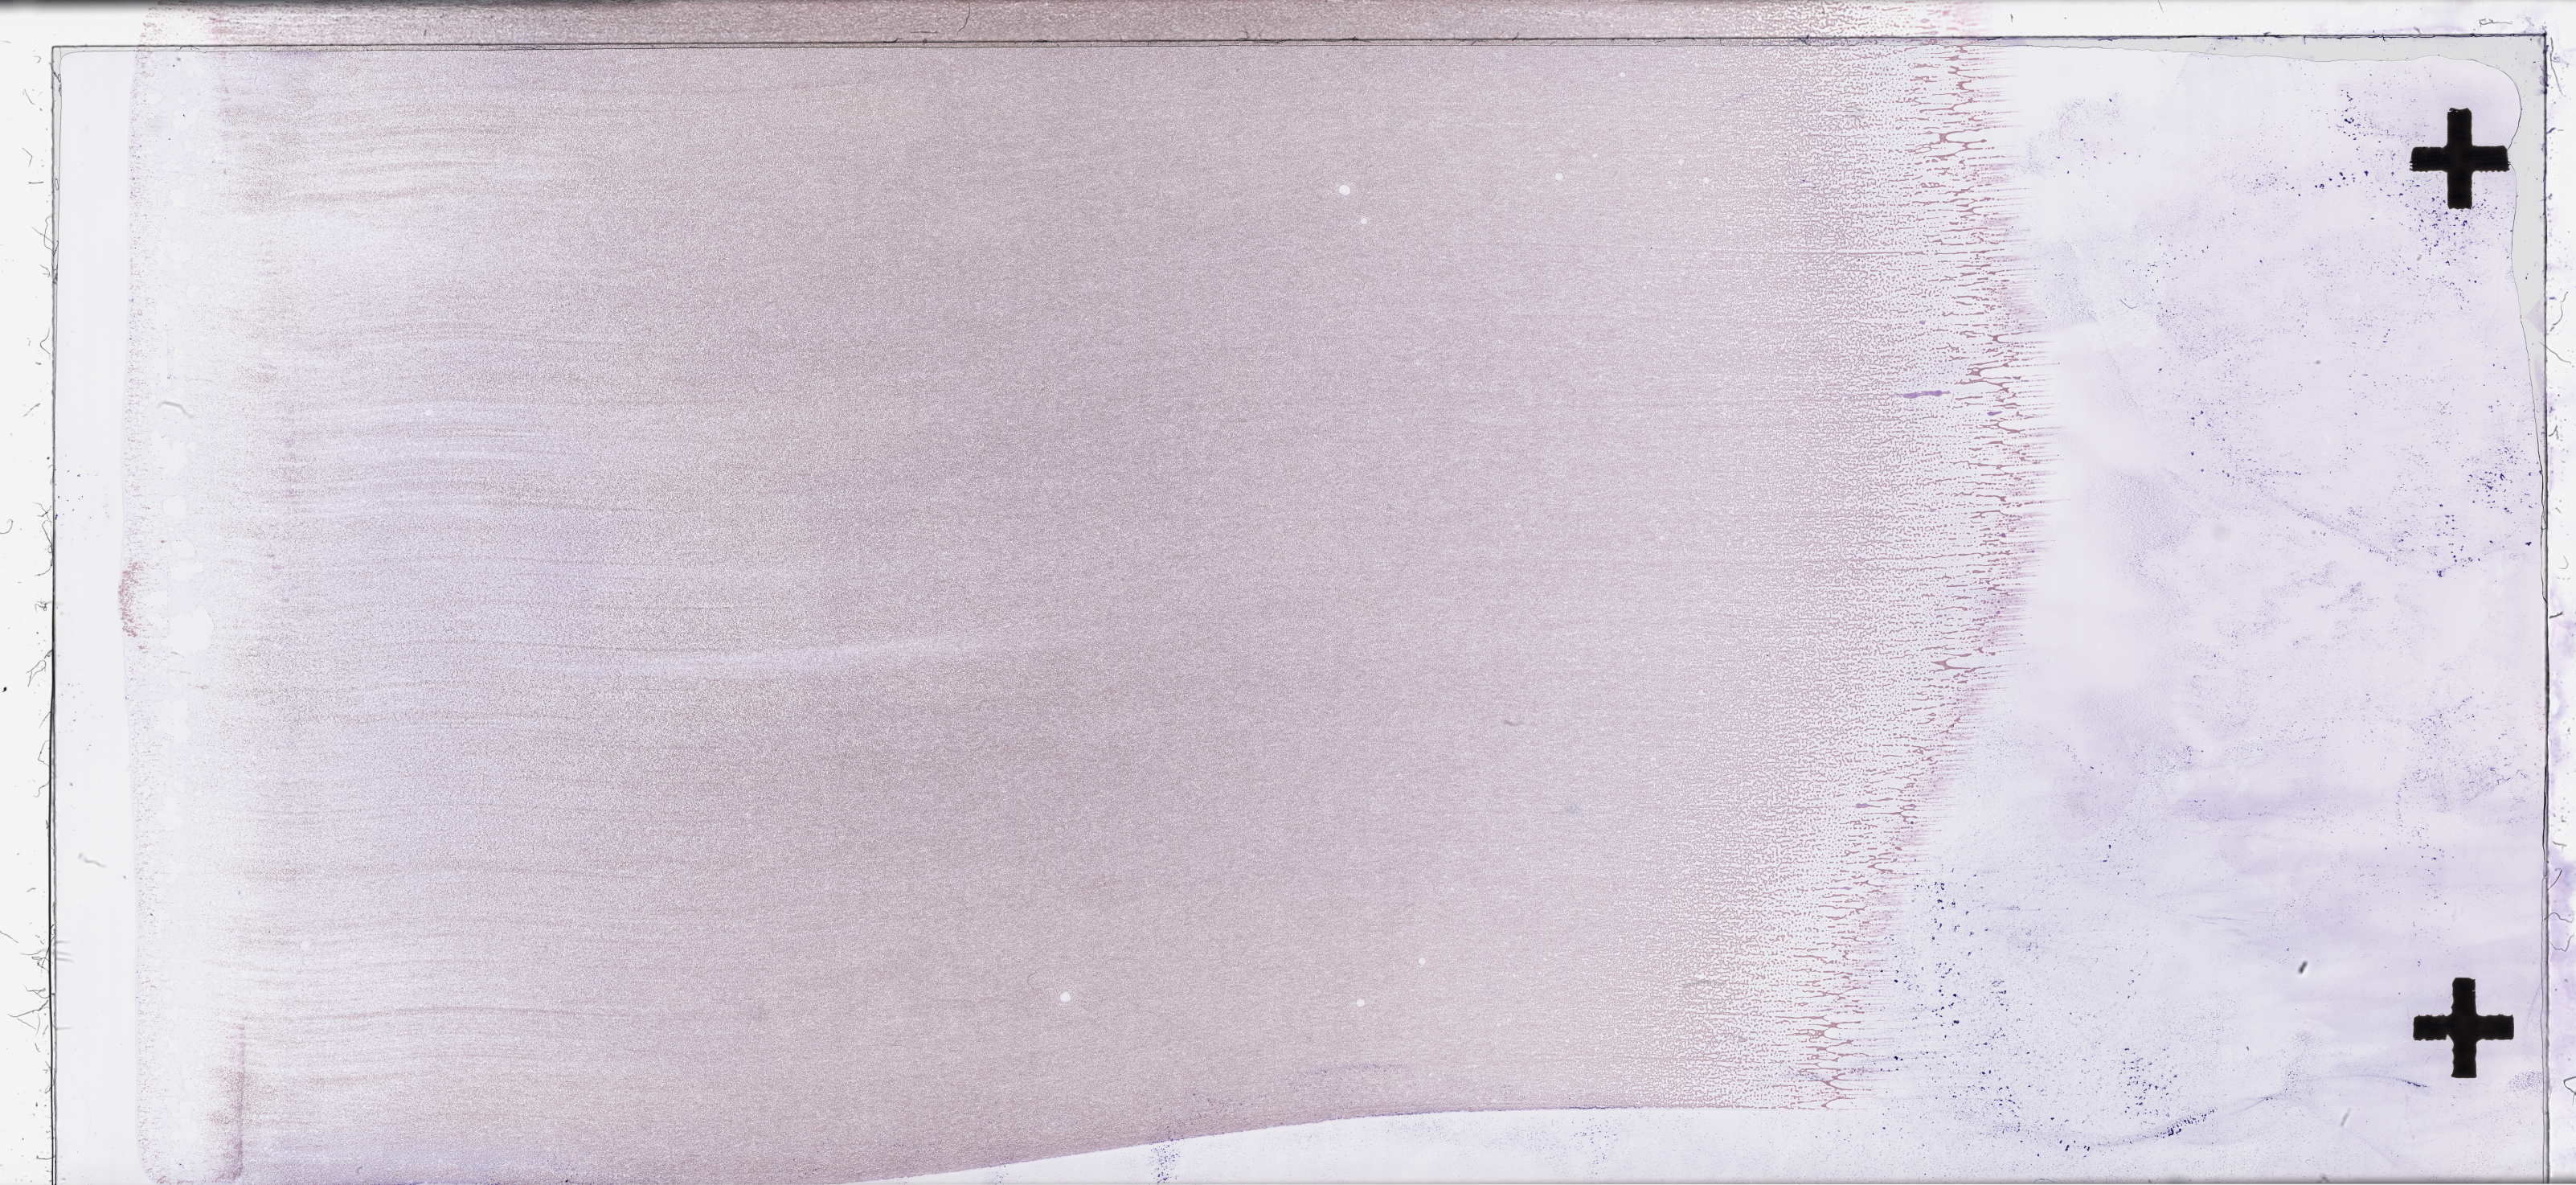
Wright-Giemsa-stained bone marrow smear, whole-slide image, a low-resolution overview of the entire scanned area, about 51.8 x 23.8 mm, EDTA-anticoagulated smear, specimen time point: collected at disease progression. Patient sex: female.
Patient diagnosis: Acute Myeloid Leukemia Not Otherwise Specified.